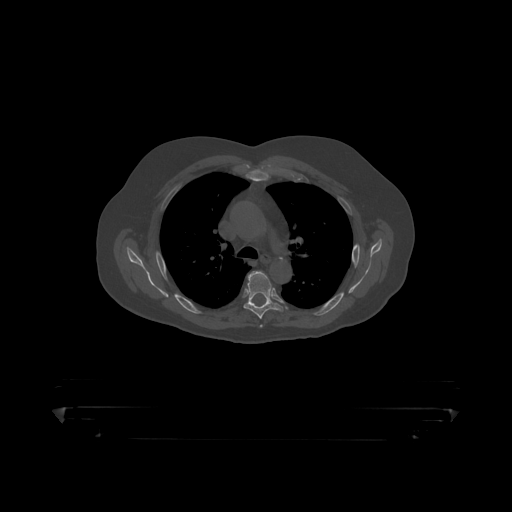
CT including the spine, one axial slice. Slice 322 of 390 in the series (ordered by position). 120 kVp. Bone window (W 1800 / L 400 HU). 512 × 512 image matrix. Male patient, age 60 years. Case-level facts recorded for this patient, not image findings: primary cancer: prostate.
Annotated regions visible in this slice (semi-automatically segmented with operator editing):
- T5 vertebra: bounding box <244,271,284,319> (left, top, right, bottom; pixels)
- T6 vertebra: <253,302,271,305>